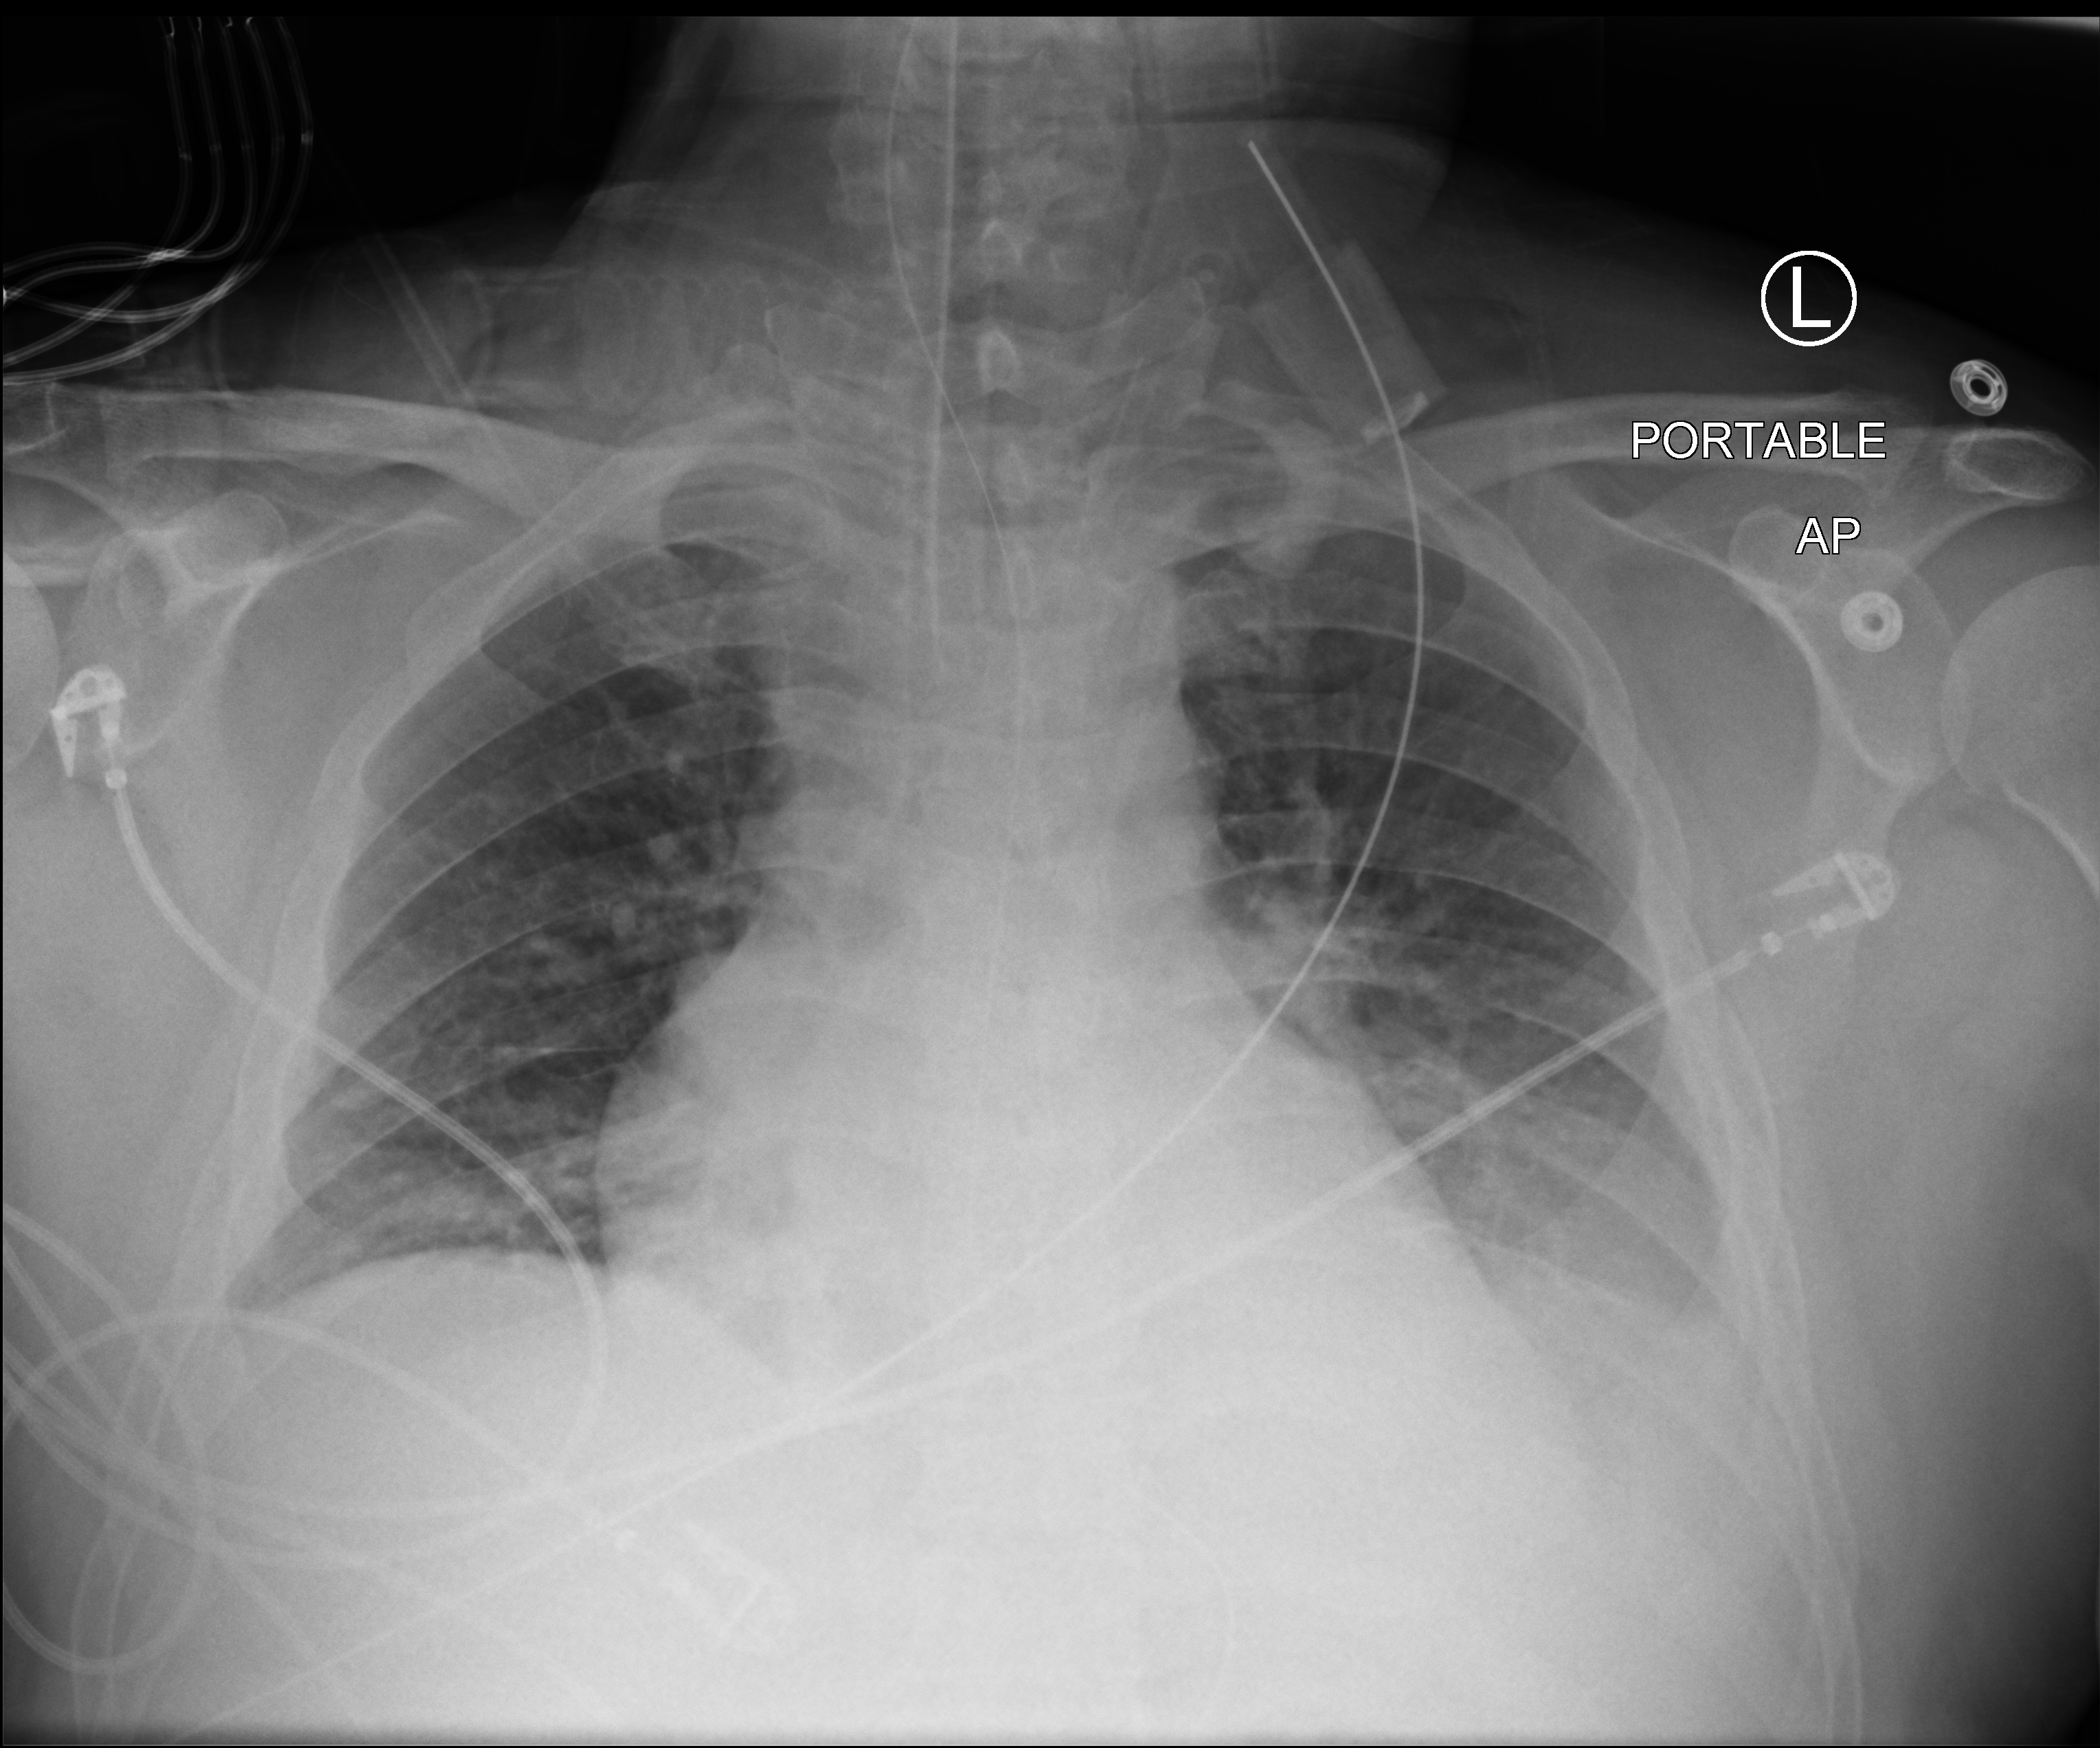
Bedside chest radiograph (computed radiography). Male patient hospitalised with COVID-19, age 18–59 years.
Admission-level facts for this patient (not findings on this image; timing relative to this image not recorded):
- admitted to intensive care during this hospital stay: yes